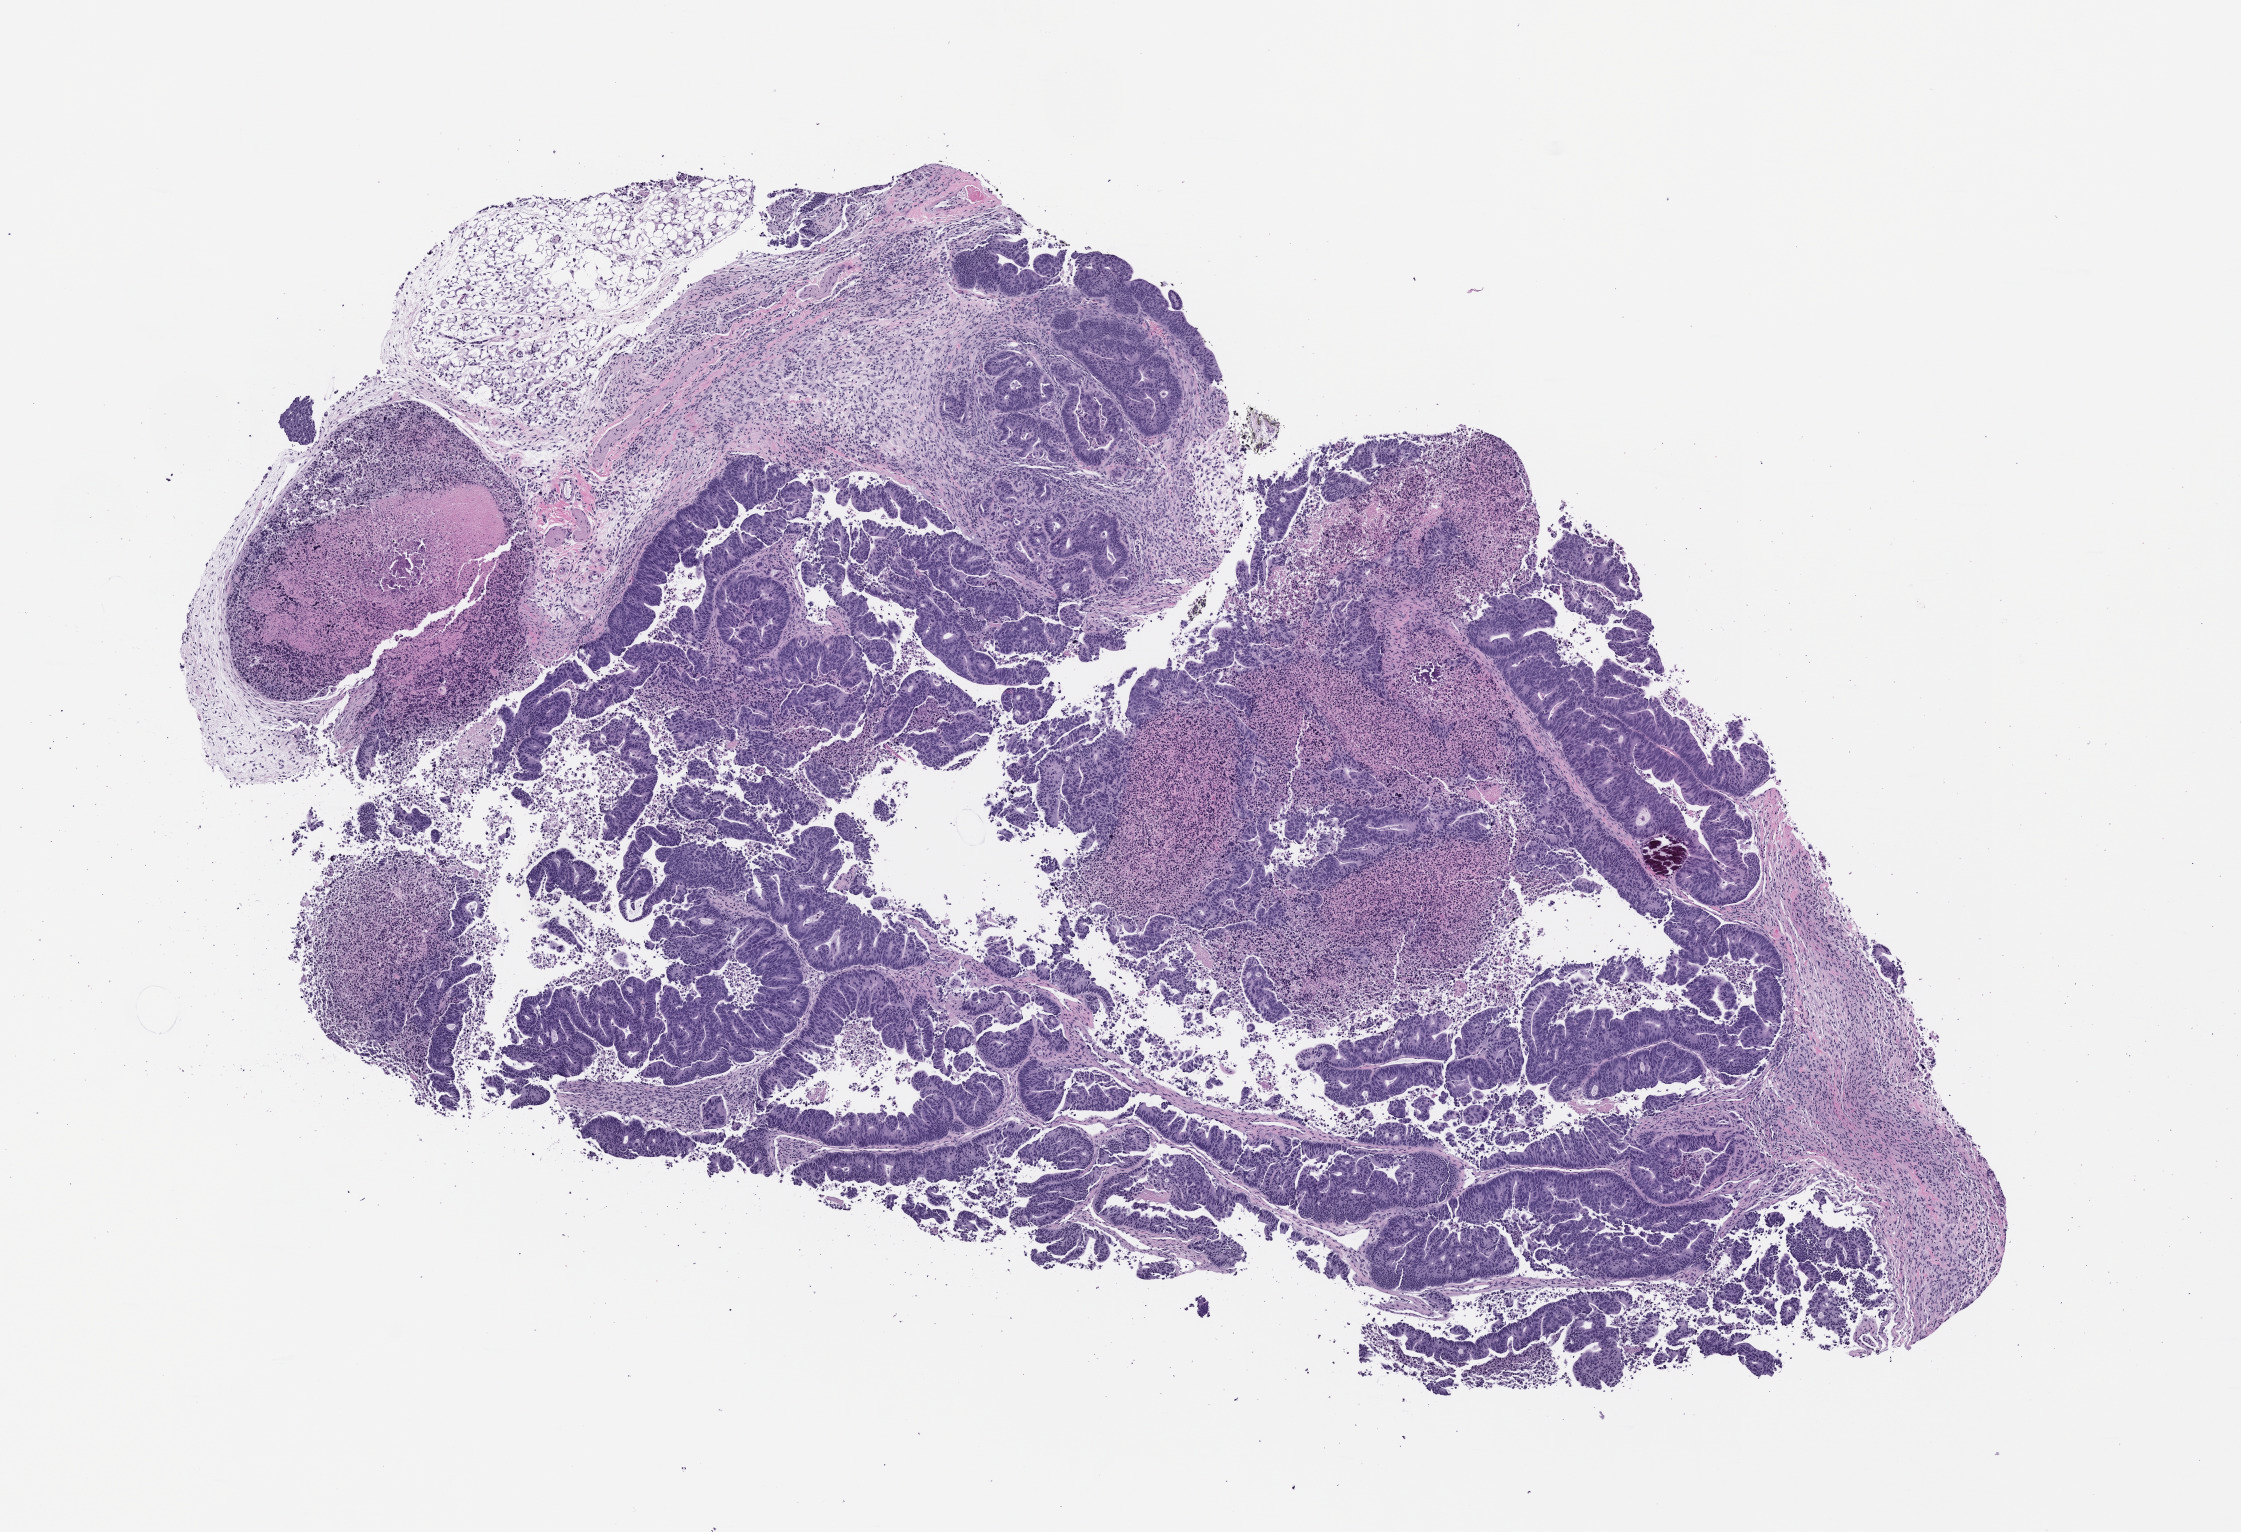
Whole-slide image, H&E: patient-derived xenograft (human tumor grown in a mouse), passage 1 — low-resolution overview of the scanned area, about 9.0 x 6.2 mm; FFPE section; originating tumor site category: rectum.
Originating patient diagnosis: Rectal Adenocarcinoma.